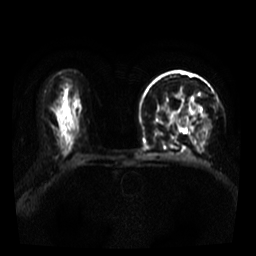
Breast MRI, one axial slice. Slice 23 of 39 in the series (ordered by position). Diffusion-weighted series; image 2 of 4 stored at this slice position (different b-values; order by instance number). 3 T. 5 mm slice thickness. 256 × 256 image matrix, field of view 320 × 320 mm. Female patient.
Structures marked on this image (outlined manually by an expert reader):
- tumour on diffusion-weighted imaging: bounding box [x1, y1, x2, y2] px = [176, 94, 207, 117]